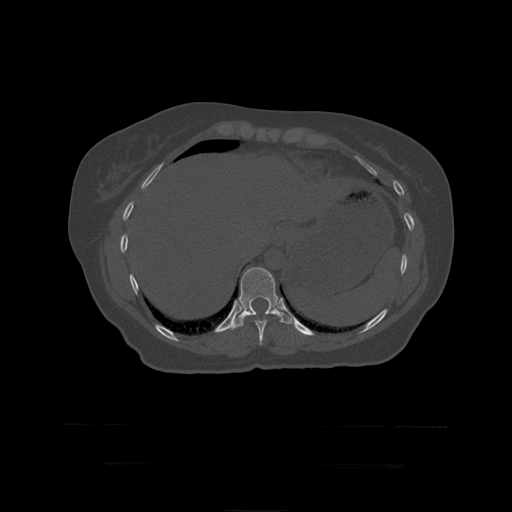
CT including the spine, one axial slice. Slice 229 of 399 in the series (ordered by position). Reconstruction kernel STANDARD. Bone window (W 1800 / L 400 HU). 512 × 512 image matrix, field of view 450 × 450 mm. Patient age 41 years. Case-level facts recorded for this patient, not image findings: primary cancer: breast.
Annotated regions visible in this slice (semi-automatic segmentation, software-assisted and operator-edited):
- T10 vertebra: bounding box (x1, y1, x2, y2) in pixels: (254, 319, 268, 345)
- T11 vertebra: (230, 267, 292, 330)